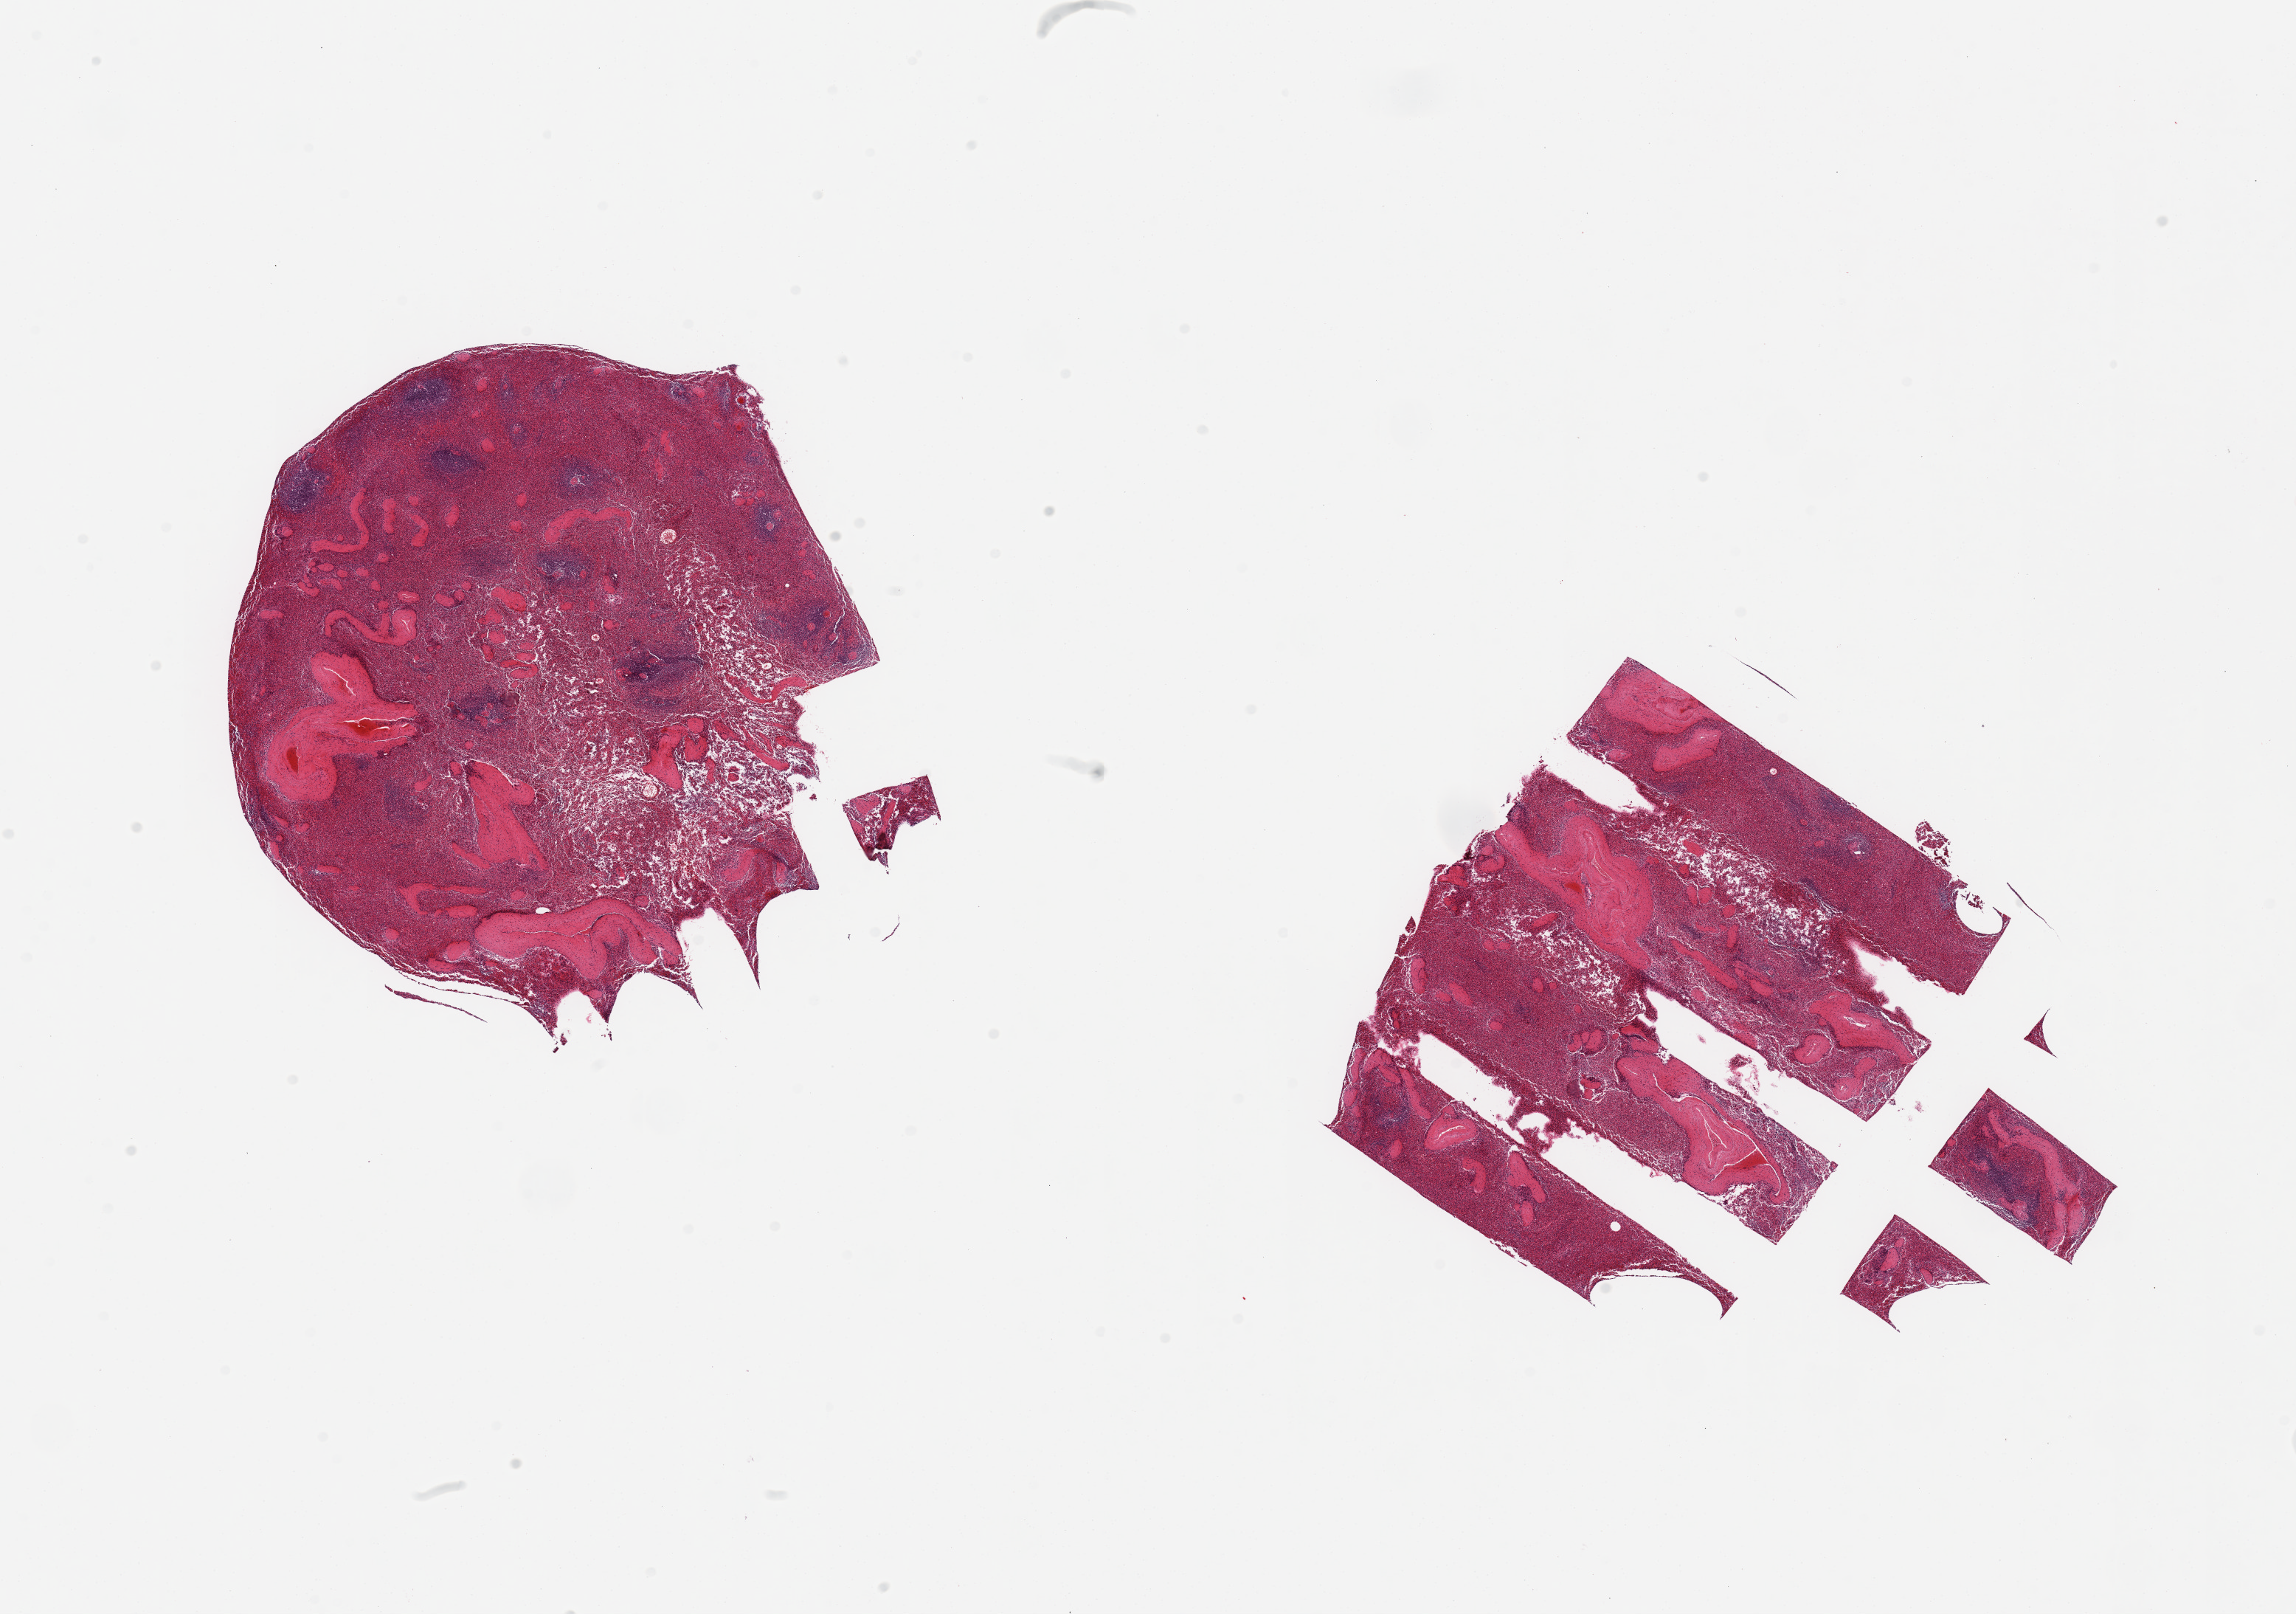
Haematoxylin and eosin whole-slide image, shown as a low-resolution overview of the whole scanned area (about 24.6 x 17.3 mm, from a 20x scan); PAXgene-fixed paraffin-embedded (PFPE) section; sampled site (target tissue): spleen; tissue donor sample. Donor sex: male.
Pathologist's review note for this sample: 2 pieces; some congestion.